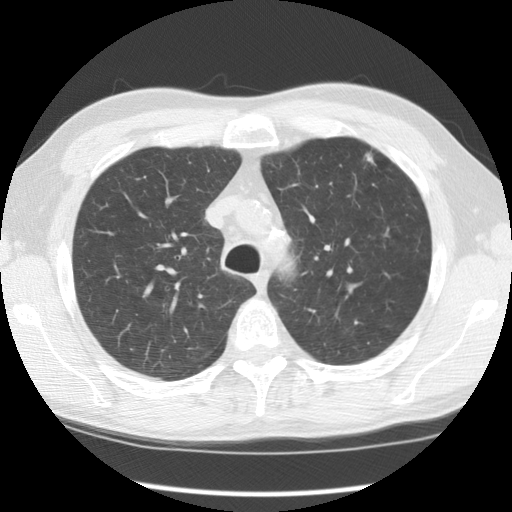
Low-dose screening chest CT, axial slice, baseline annual screen, lung window (W 1500 / L -600 HU), 2.5 mm slice thickness, standard (soft-tissue) reconstruction kernel (STANDARD), 120 kVp, slice 30 of 121 in the series, 512 × 512 image matrix, field of view 350 × 350 mm. Male, age 55 years at enrolment. Current smoker at enrolment.
Expert-annotated lung lesion, bounding box [x1, y1, x2, y2] px = [351, 138, 396, 182]. The exam's reader record, not a measurement of the box and not confirmed to be the same lesion: non-calcified nodule or mass ≥4 mm, left upper lobe, 5 × 5 mm, poorly defined margins, soft tissue attenuation. Participant outcome: lung cancer diagnosed 159 days after this screen — adenocarcinoma, NOS, left upper lobe, moderately differentiated (G2), stage IA (AJCC 6th edition), 8 mm at pathology.